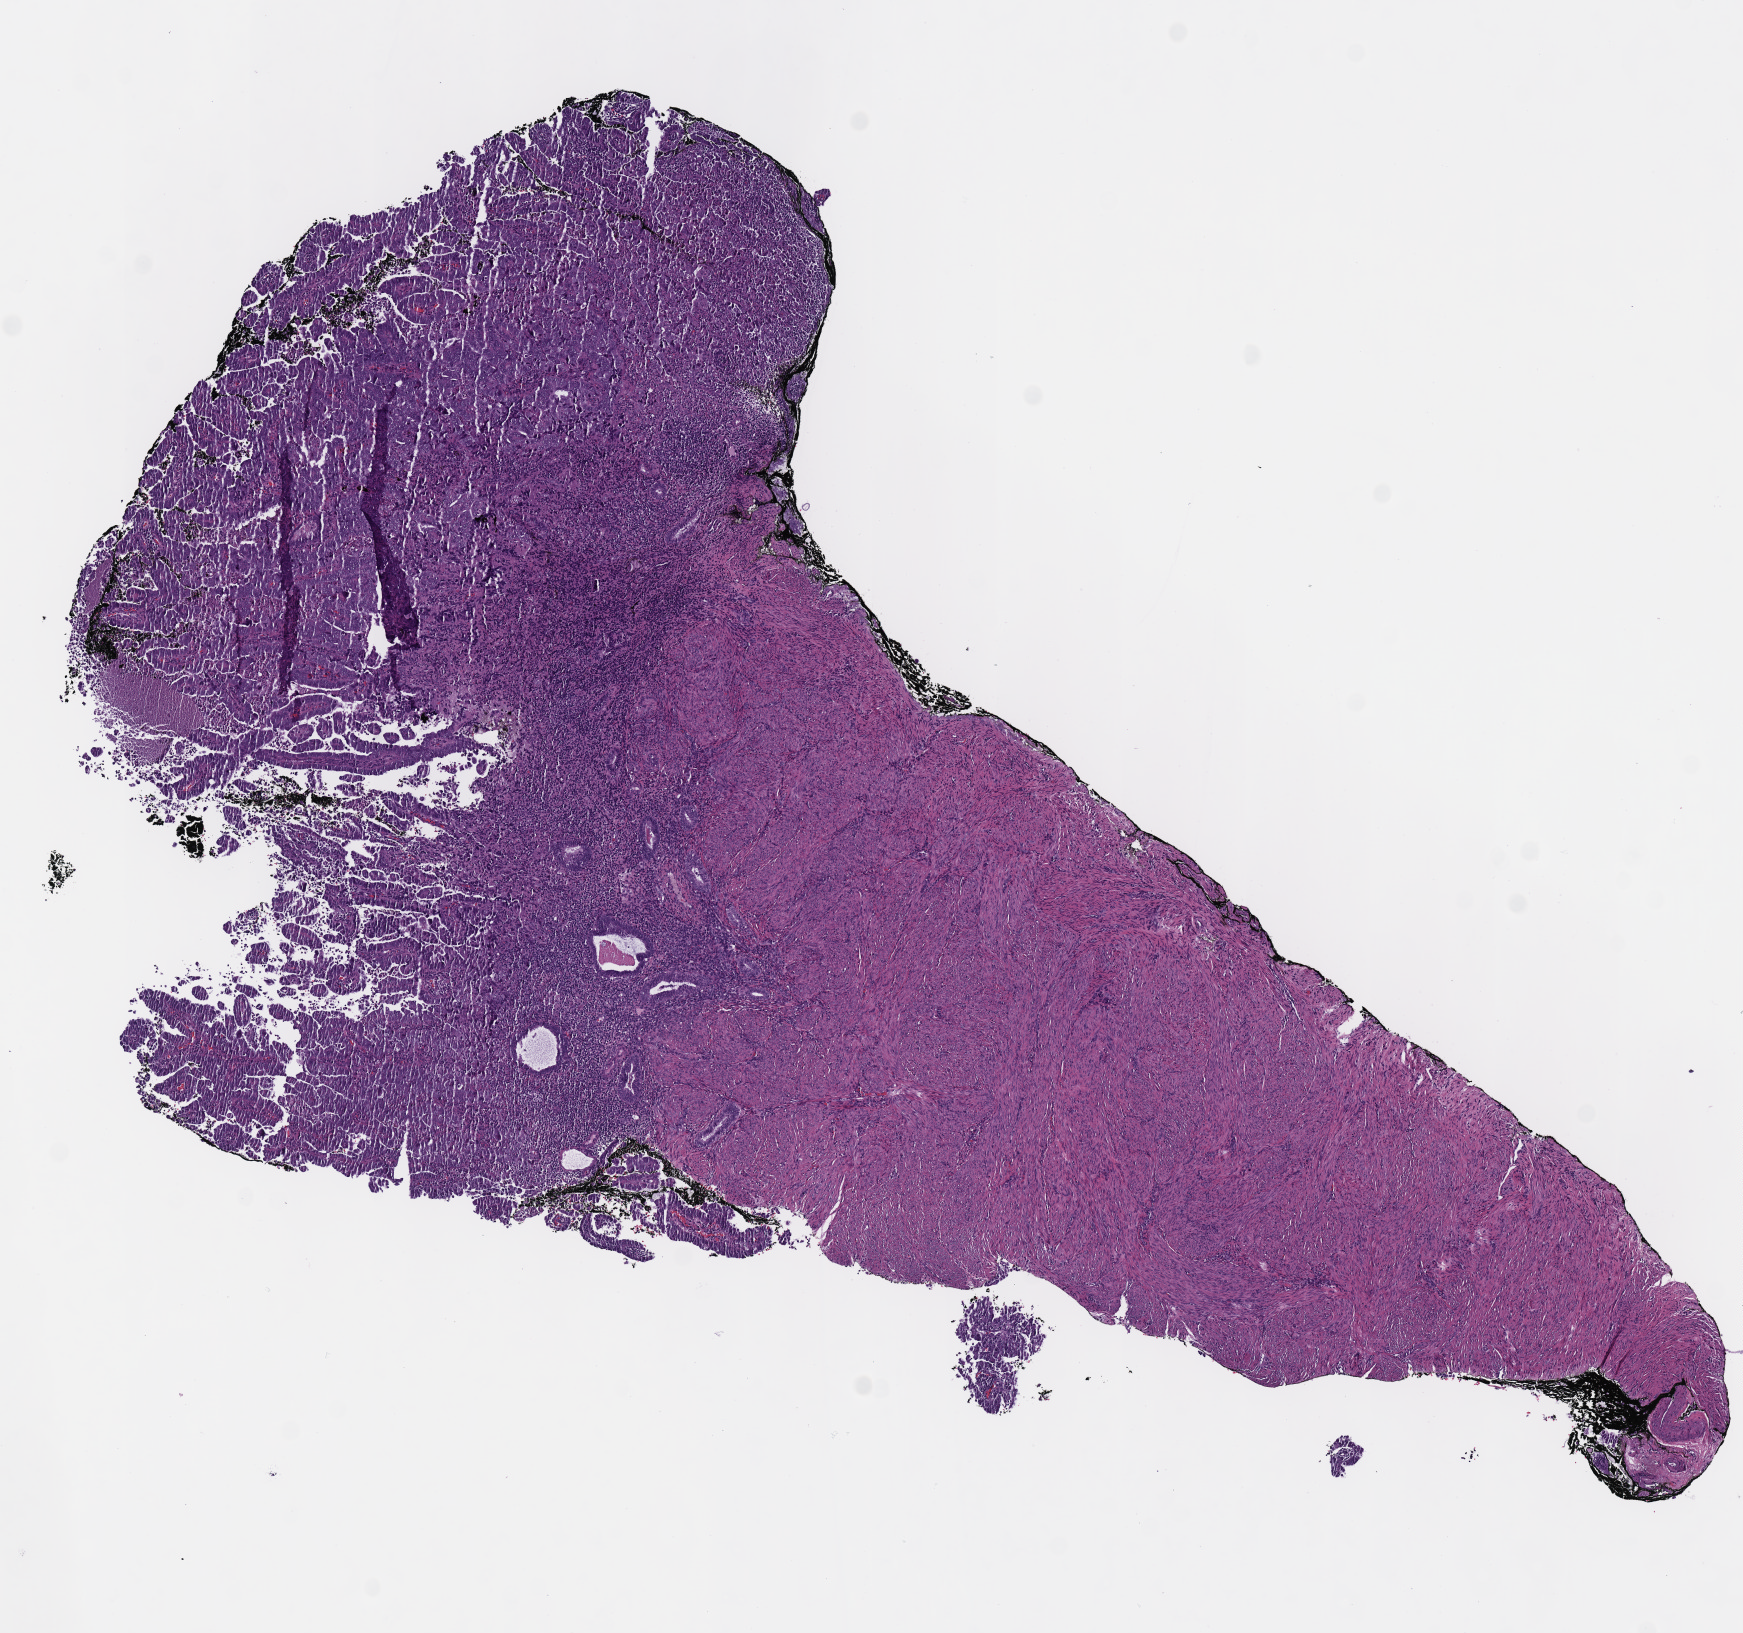
Digitized Hematoxylin and eosin (H&E) stained tissue section (whole slide), shown as a low-resolution overview of the whole scanned area (about 6.9 x 6.4 mm, from a 40x scan). Formalin-fixed paraffin-embedded (FFPE) diagnostic section. Uterus, primary tumour sample. Female, age 57 years at initial diagnosis. Histologic grade: G3 (poorly differentiated).
- pathologic diagnosis: Serous cystadenocarcinoma, NOS (endometrium)
- FIGO stage: IIIA